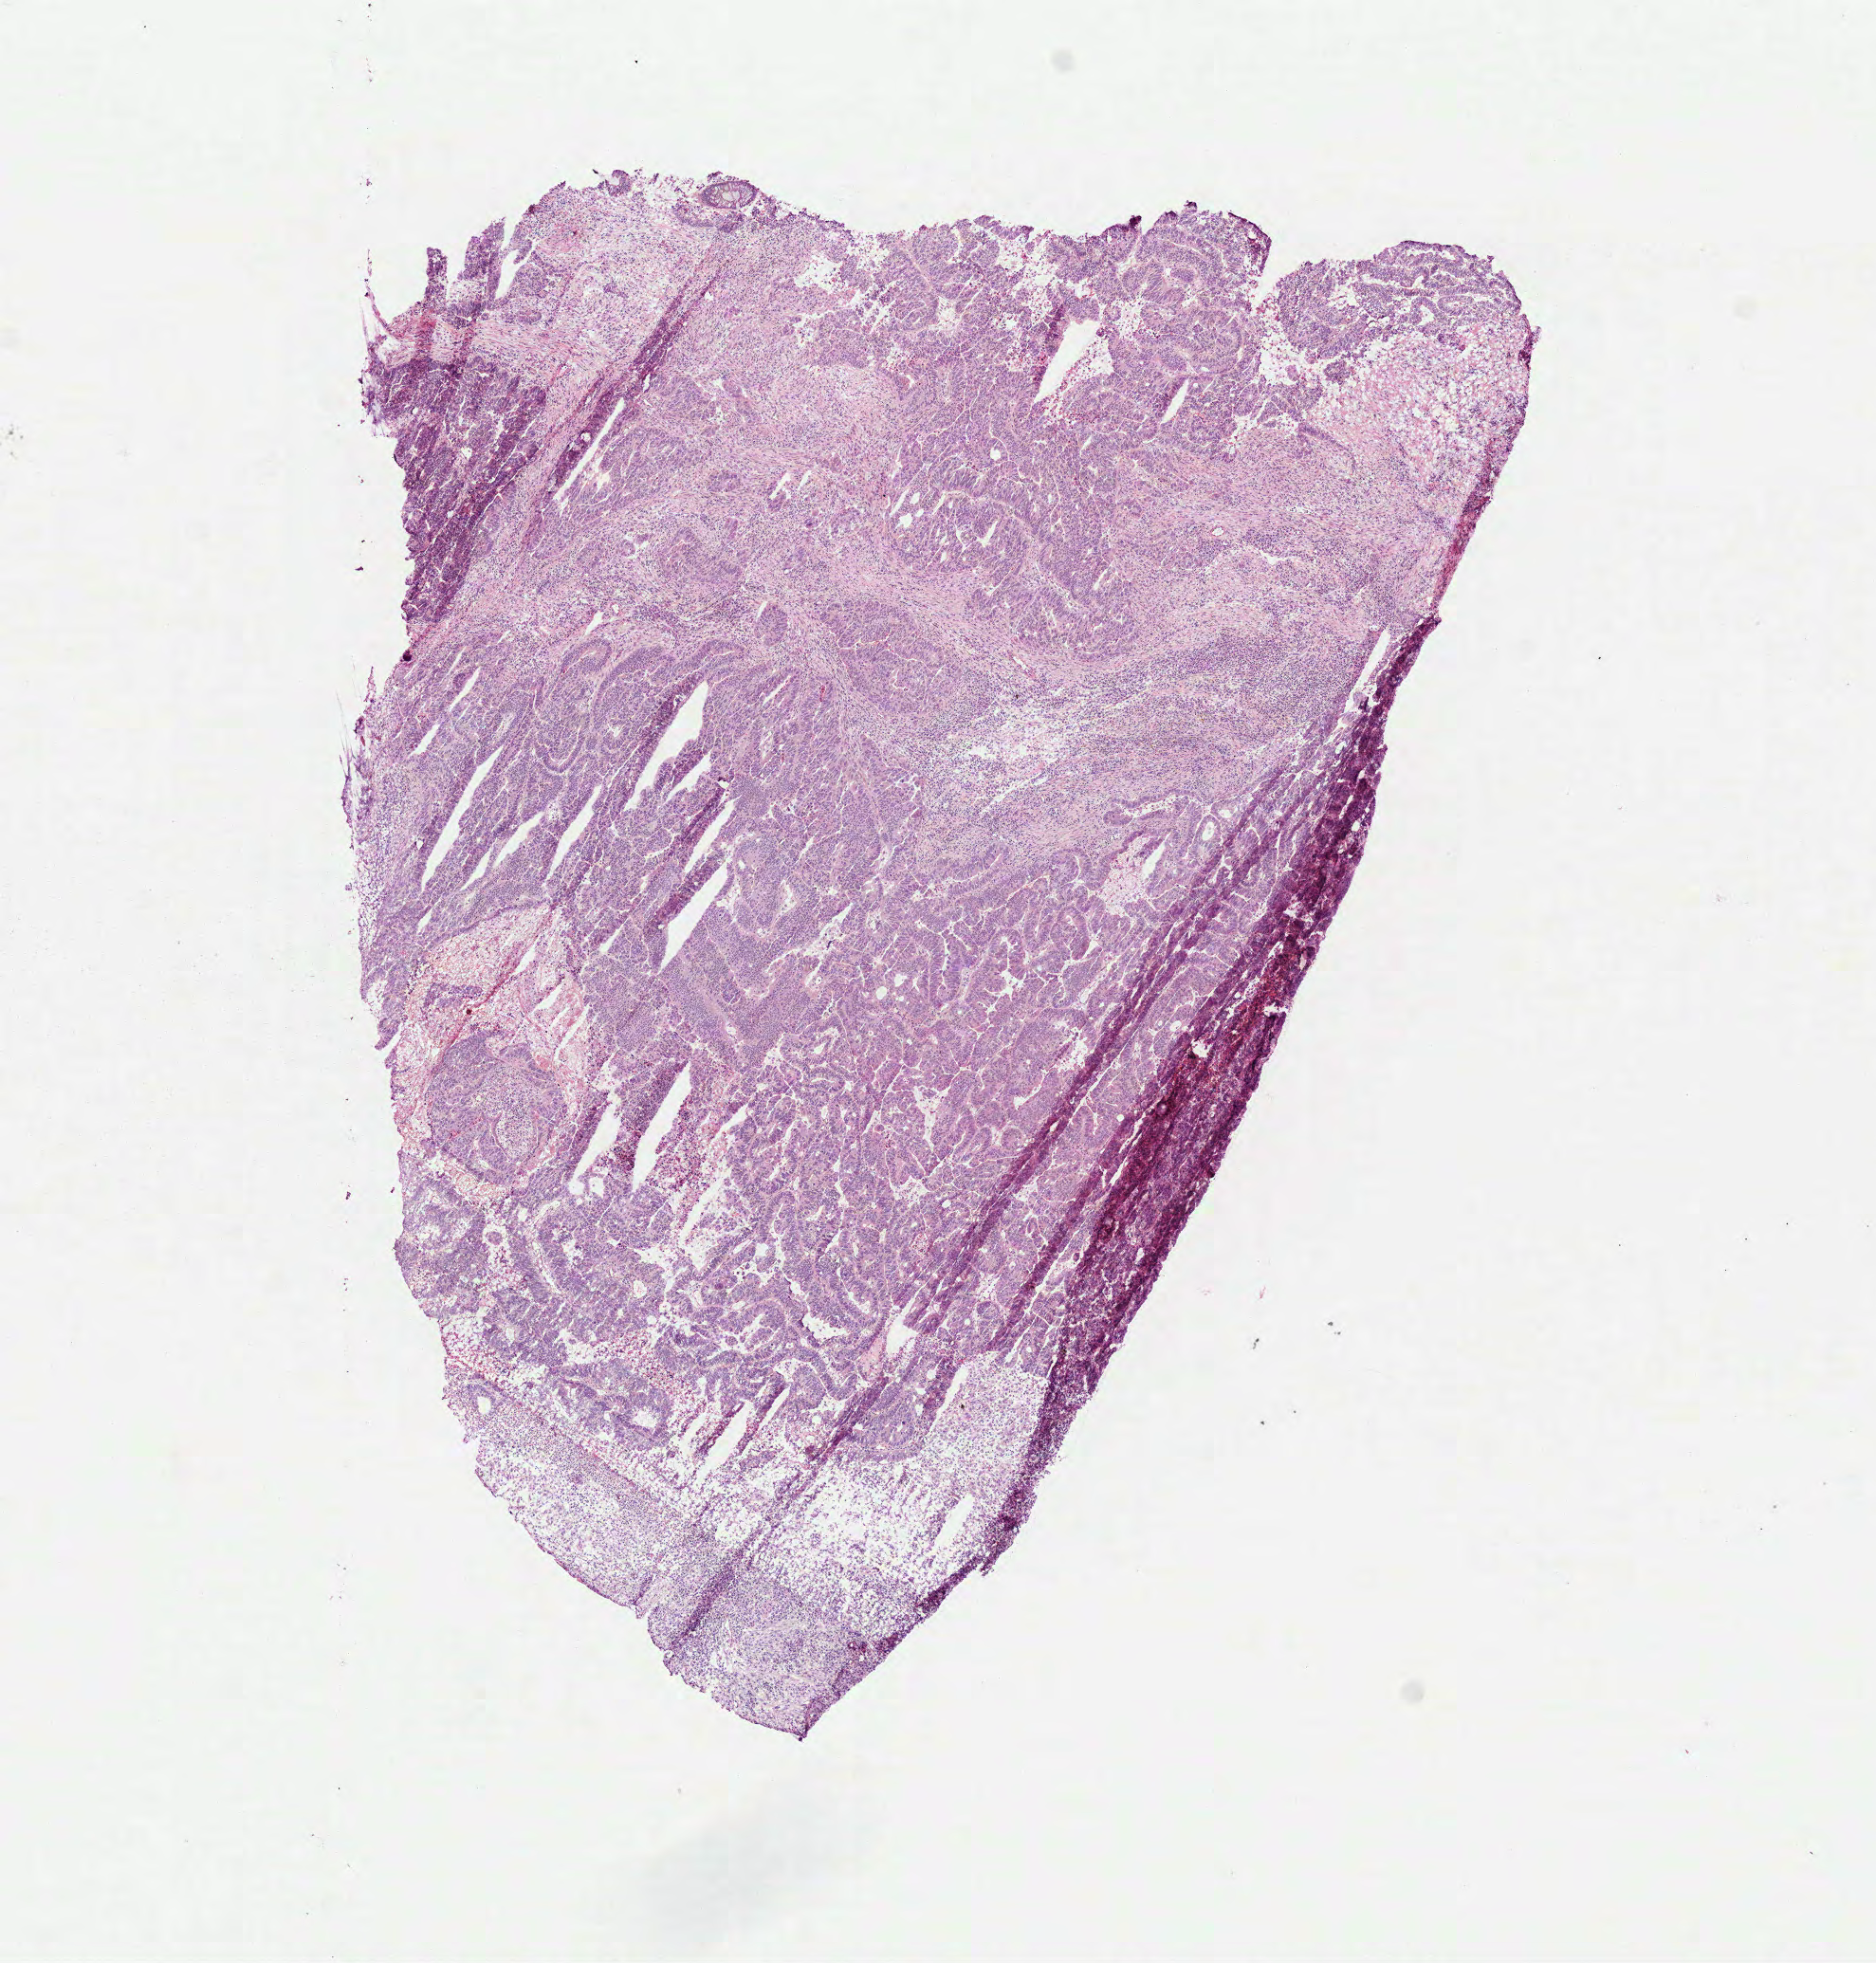
Hematoxylin and eosin (H&E) stained whole-slide image — whole scanned area (about 8.0 x 8.3 mm, acquisition: 40x scan) shown as a low-resolution overview, frozen section, sample: primary tumour, colon. Male patient; age at initial diagnosis 68 years. Composition of this section per pathologist review: tumour cells 75%, tumour nuclei 85%, normal cells 0%, stromal cells 17%, necrosis 8%. Infiltration values recorded for this section: lymphocyte infiltration 7%, monocyte infiltration 0%, neutrophil infiltration 1%.
AJCC pathologic stage: IIA (7th edition). Diagnosis: Adenocarcinoma, NOS (sigmoid colon).